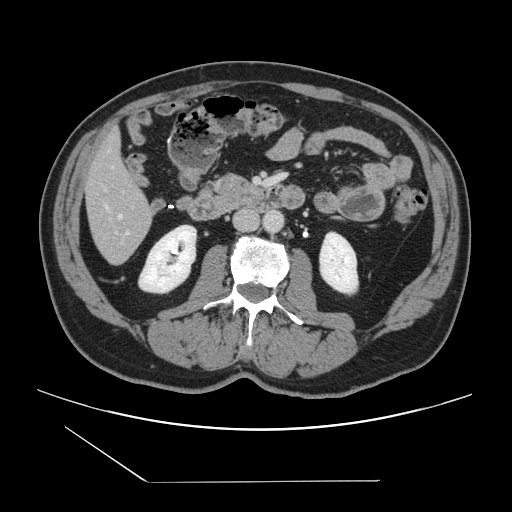
Contrast-enhanced abdominal CT, one axial slice; slice 39 of 157 in the series (ordered by position); soft-tissue window (W 400 / L 40 HU); 2.5 mm slice thickness; 512 × 512 image matrix, field of view 407 × 407 mm. Male patient, age 61 years. From the clinical record (not read from this slice): diagnosis: colorectal cancer liver metastases, imaged before liver resection; multiple liver metastases: yes; largest metastasis: 5.5 cm.
Structures marked on this image (expert manual segmentation):
- hepatic veins: bounding box (x1, y1, x2, y2) in pixels: (119, 215, 122, 218)
- liver: (85, 132, 154, 264)
- planned liver remnant (the part of the liver to remain after resection): (85, 132, 149, 218)
- portal vein (with intrahepatic branches): (126, 231, 129, 234)